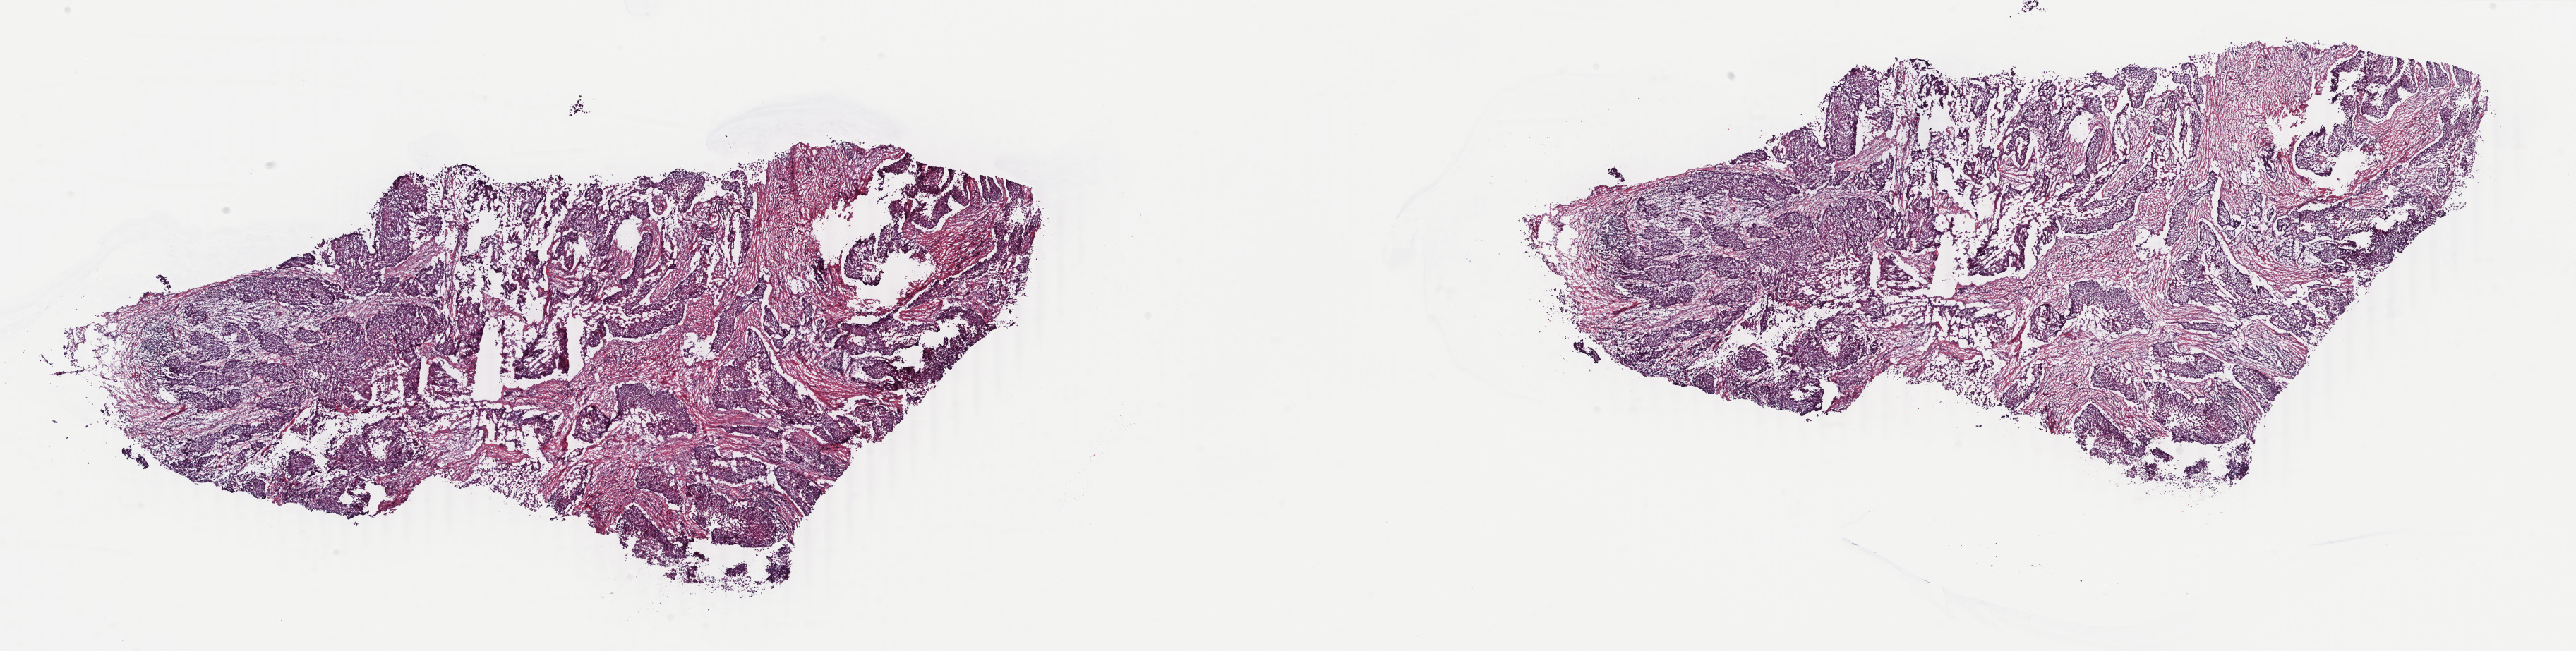
H&E-stained whole-slide image, shown as a low-resolution overview of the whole scanned area (about 29.0 x 7.3 mm, acquisition: 40x scan). Frozen section from the top of the tissue portion. Sample: primary tumour, lung. Patient: female, age at initial diagnosis 70 years. Pathologist review of this section (percent, as recorded): tumour cells 100%, tumour nuclei 75%, normal cells 0%, stromal cells 0%, necrosis 0%. Infiltration values recorded for this section: lymphocyte infiltration 0%, monocyte infiltration 0%, neutrophil infiltration 0%.
- pathologic diagnosis: Squamous cell carcinoma, keratinizing, NOS (upper lobe, lung)
- AJCC pathologic stage: IIIA